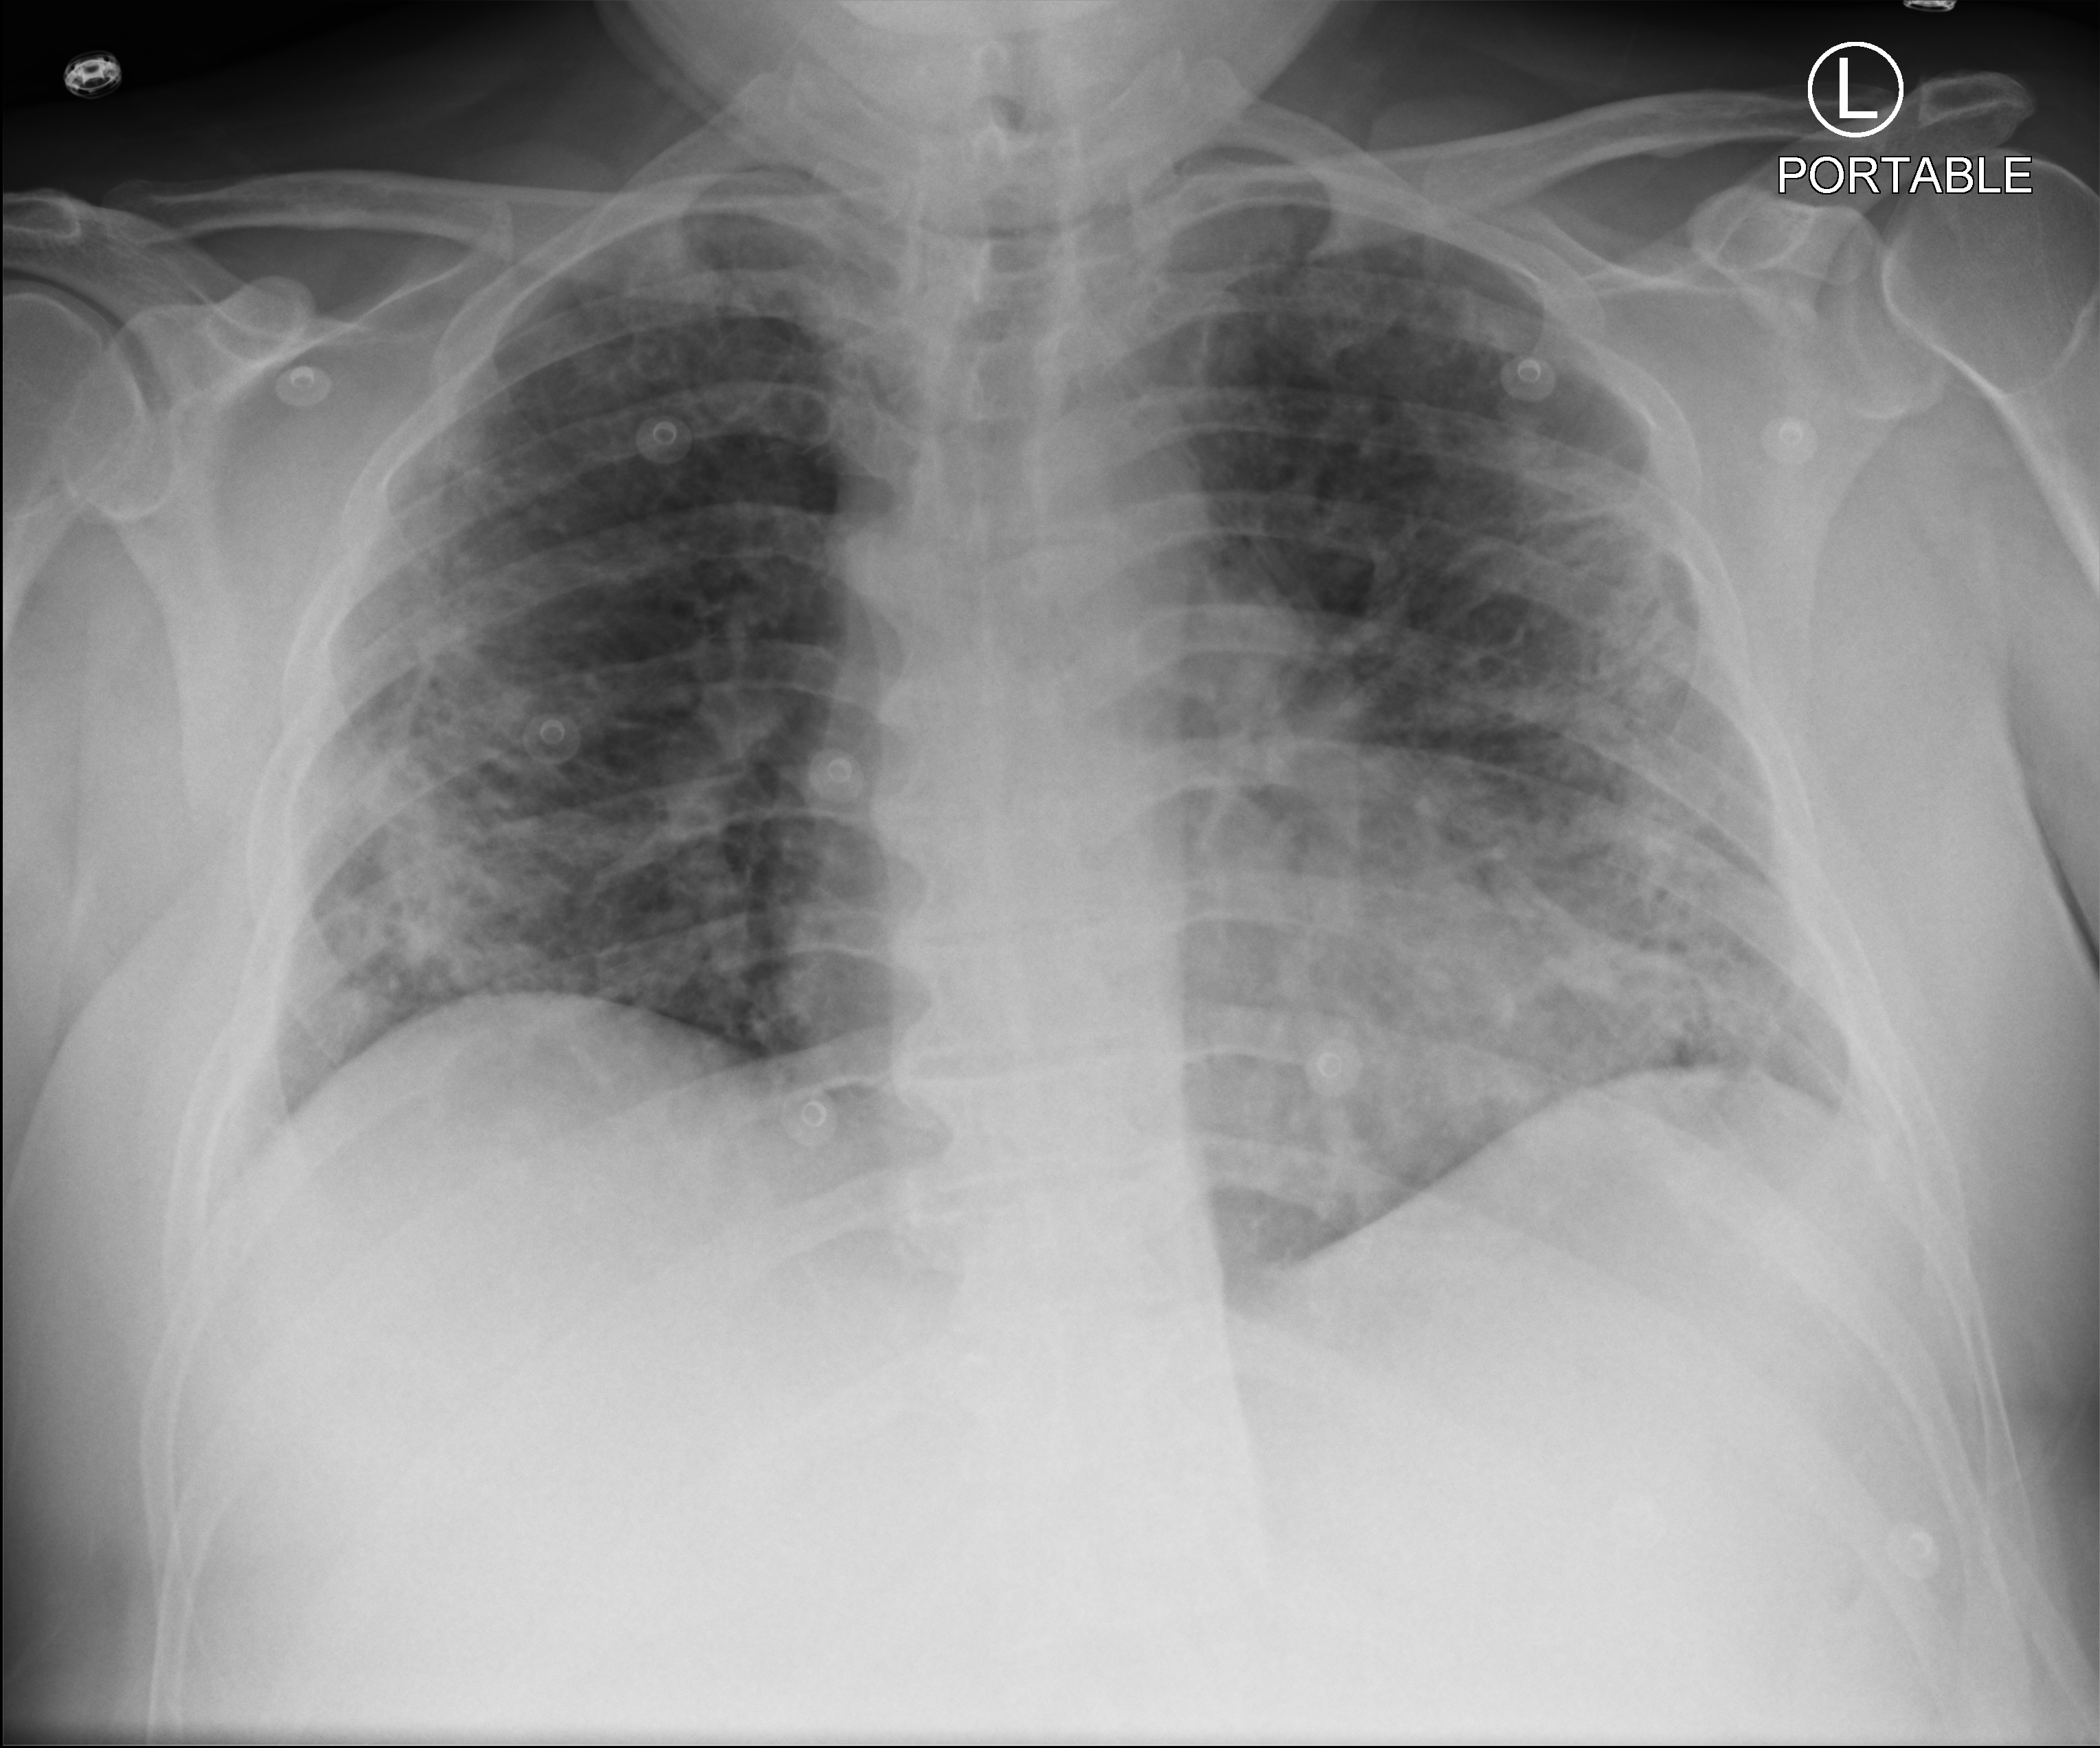
Chest X-ray (portable); anteroposterior (AP) projection. Male patient hospitalised with COVID-19, age 18–59 years.
From the hospital-stay record, not from the radiograph (when in the stay this image was taken is not recorded): diabetes (admission record): yes; admitted to intensive care during this hospital stay: yes.